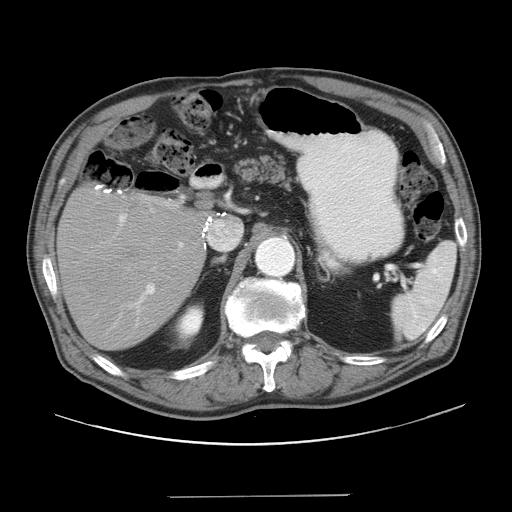
Contrast-enhanced abdominal CT, one axial slice. Reconstruction kernel STANDARD. 120 kVp. Intravenous contrast given. Soft-tissue window (W 400 / L 40 HU). 5 mm slice thickness. 512 × 512 image matrix, field of view 420 × 420 mm. Male patient, age 75 years. From the clinical record (not read from this slice): diagnosis: colorectal cancer liver metastases, imaged before liver resection; multiple liver metastases: no; largest metastasis: 5.2 cm; disease in both lobes: no.
Annotated regions visible in this slice (manually delineated by an expert):
- liver: box from (x=59, y=190) to (x=205, y=350) px
- planned liver remnant (the part of the liver to remain after resection): (x=60, y=190)–(x=204, y=350)
- portal vein (with intrahepatic branches): (x=106, y=203)–(x=184, y=334)